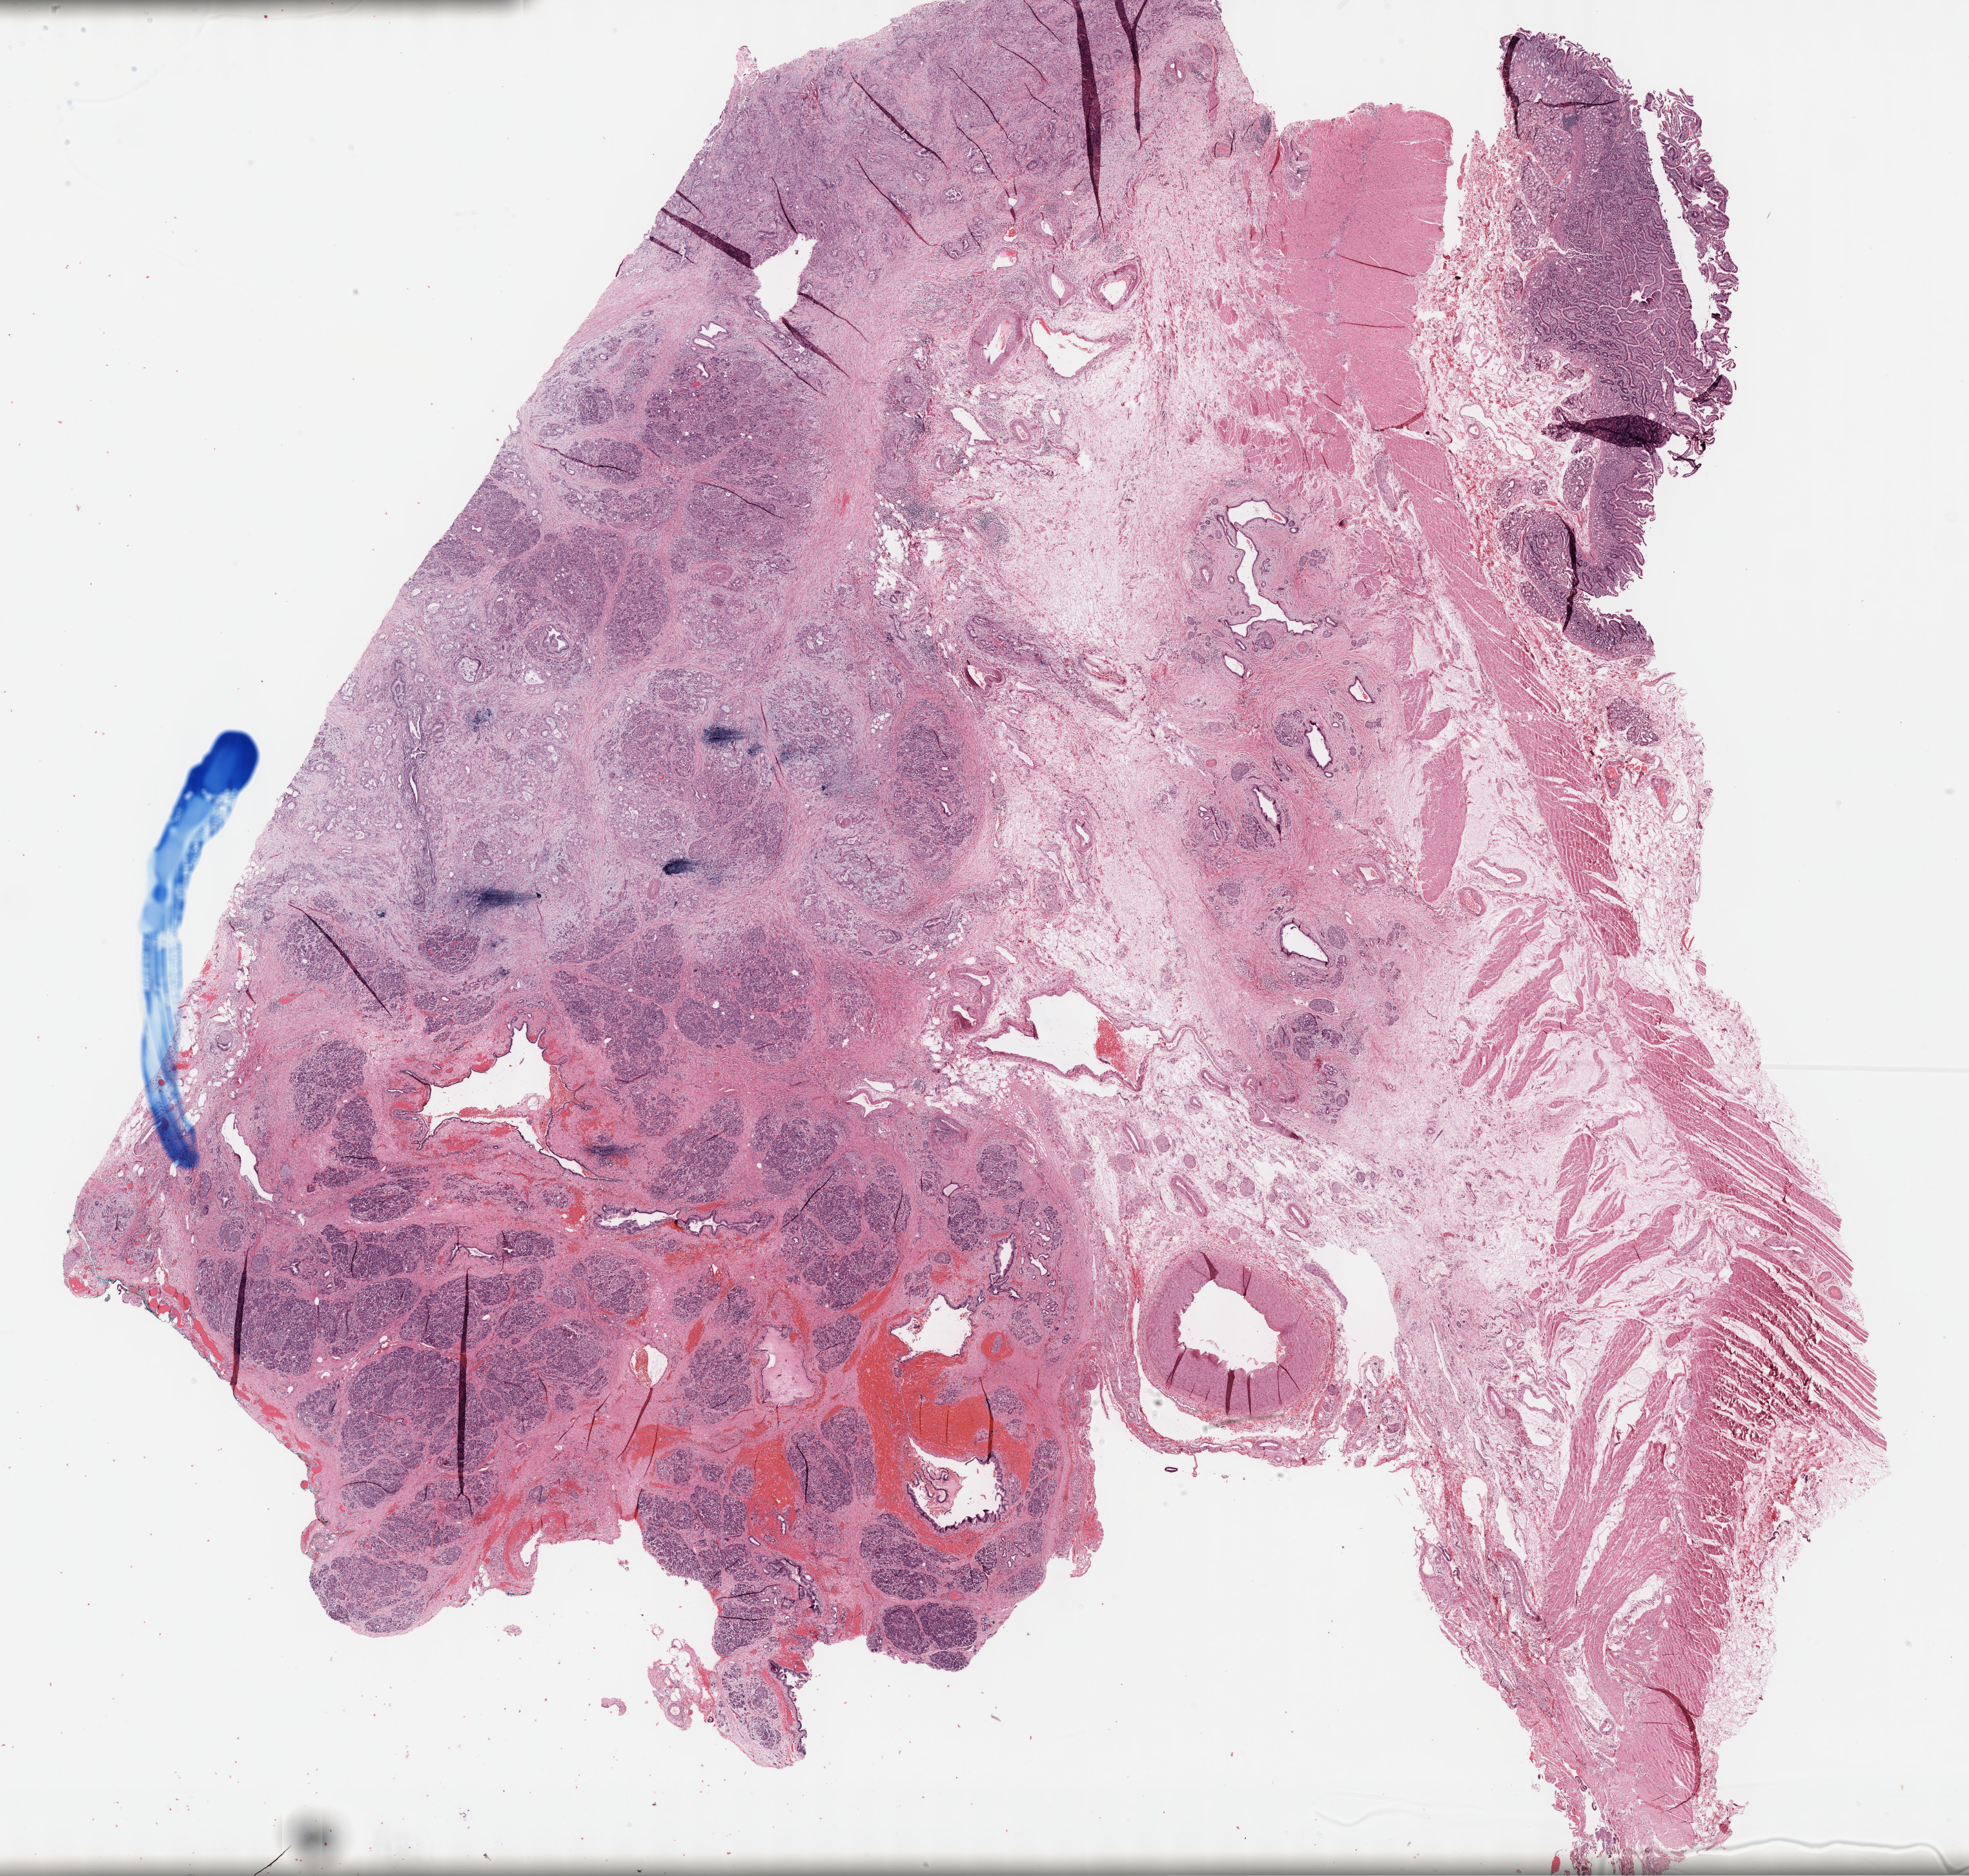
Digitized Hematoxylin and eosin (H&E) stained tissue section (whole slide), low-resolution overview of the scanned area, about 24.7 x 23.5 mm (acquisition: 40x scan); FFPE section; sample: primary tumour, pancreas. Patient: female, age at initial diagnosis 63 years.
Diagnosis: Infiltrating duct carcinoma, NOS (head of pancreas).